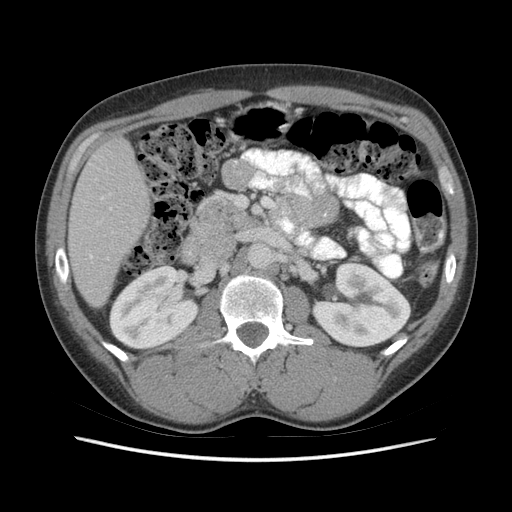
Contrast-enhanced abdominal CT (liver protocol), one axial slice; position 21 of 73 along the scan axis; reconstruction kernel STANDARD; soft-tissue window (W 400 / L 40 HU); 2.5 mm slice thickness; 512 × 512 image matrix, field of view 360 × 360 mm. Case-level facts recorded for this patient, not image findings: diagnosis: hepatocellular carcinoma (patient treated with transarterial chemoembolisation; whether this scan precedes or follows treatment is not stated here); TNM stage (as recorded): Stage-IIIA; Child-Pugh class: A; tumour nodularity: multinodular; tumour size: 6.6 cm.
Structures marked on this image (semi-automatically segmented with operator editing):
- liver parenchyma outside the tumour (the mass and vessels are separate outlines, so this box may not span the whole liver): bounding box (x1, y1, x2, y2) in pixels: (68, 138, 150, 306)
- liver vessels: (90, 197, 112, 258)